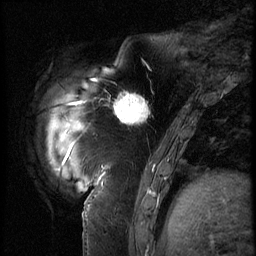
Breast MRI (dynamic contrast-enhanced), one sagittal slice. Position 15 of 62 along the scan axis. 3 images stored at this slice position (order not interpretable as contrast timing). 1.5 T. TE 4.2 ms, TR 9 ms. 256 × 256 image matrix, field of view 180 × 180 mm. Female patient, age 57 years. From the clinical record (not read from this slice): setting: breast cancer imaged before/during neoadjuvant chemotherapy; receptor status: triple-negative.
Structures marked on this image (semi-automatic segmentation, software-assisted and operator-edited):
- analysis volume of interest (the breast-tissue region the enhancement analysis was run in; not a lesion): box from (x=105, y=84) to (x=158, y=135) px
- tumour enhancement mask (voxels above the 140 % enhancement threshold inside the analysis volume of interest): (x=114, y=90)–(x=151, y=125)